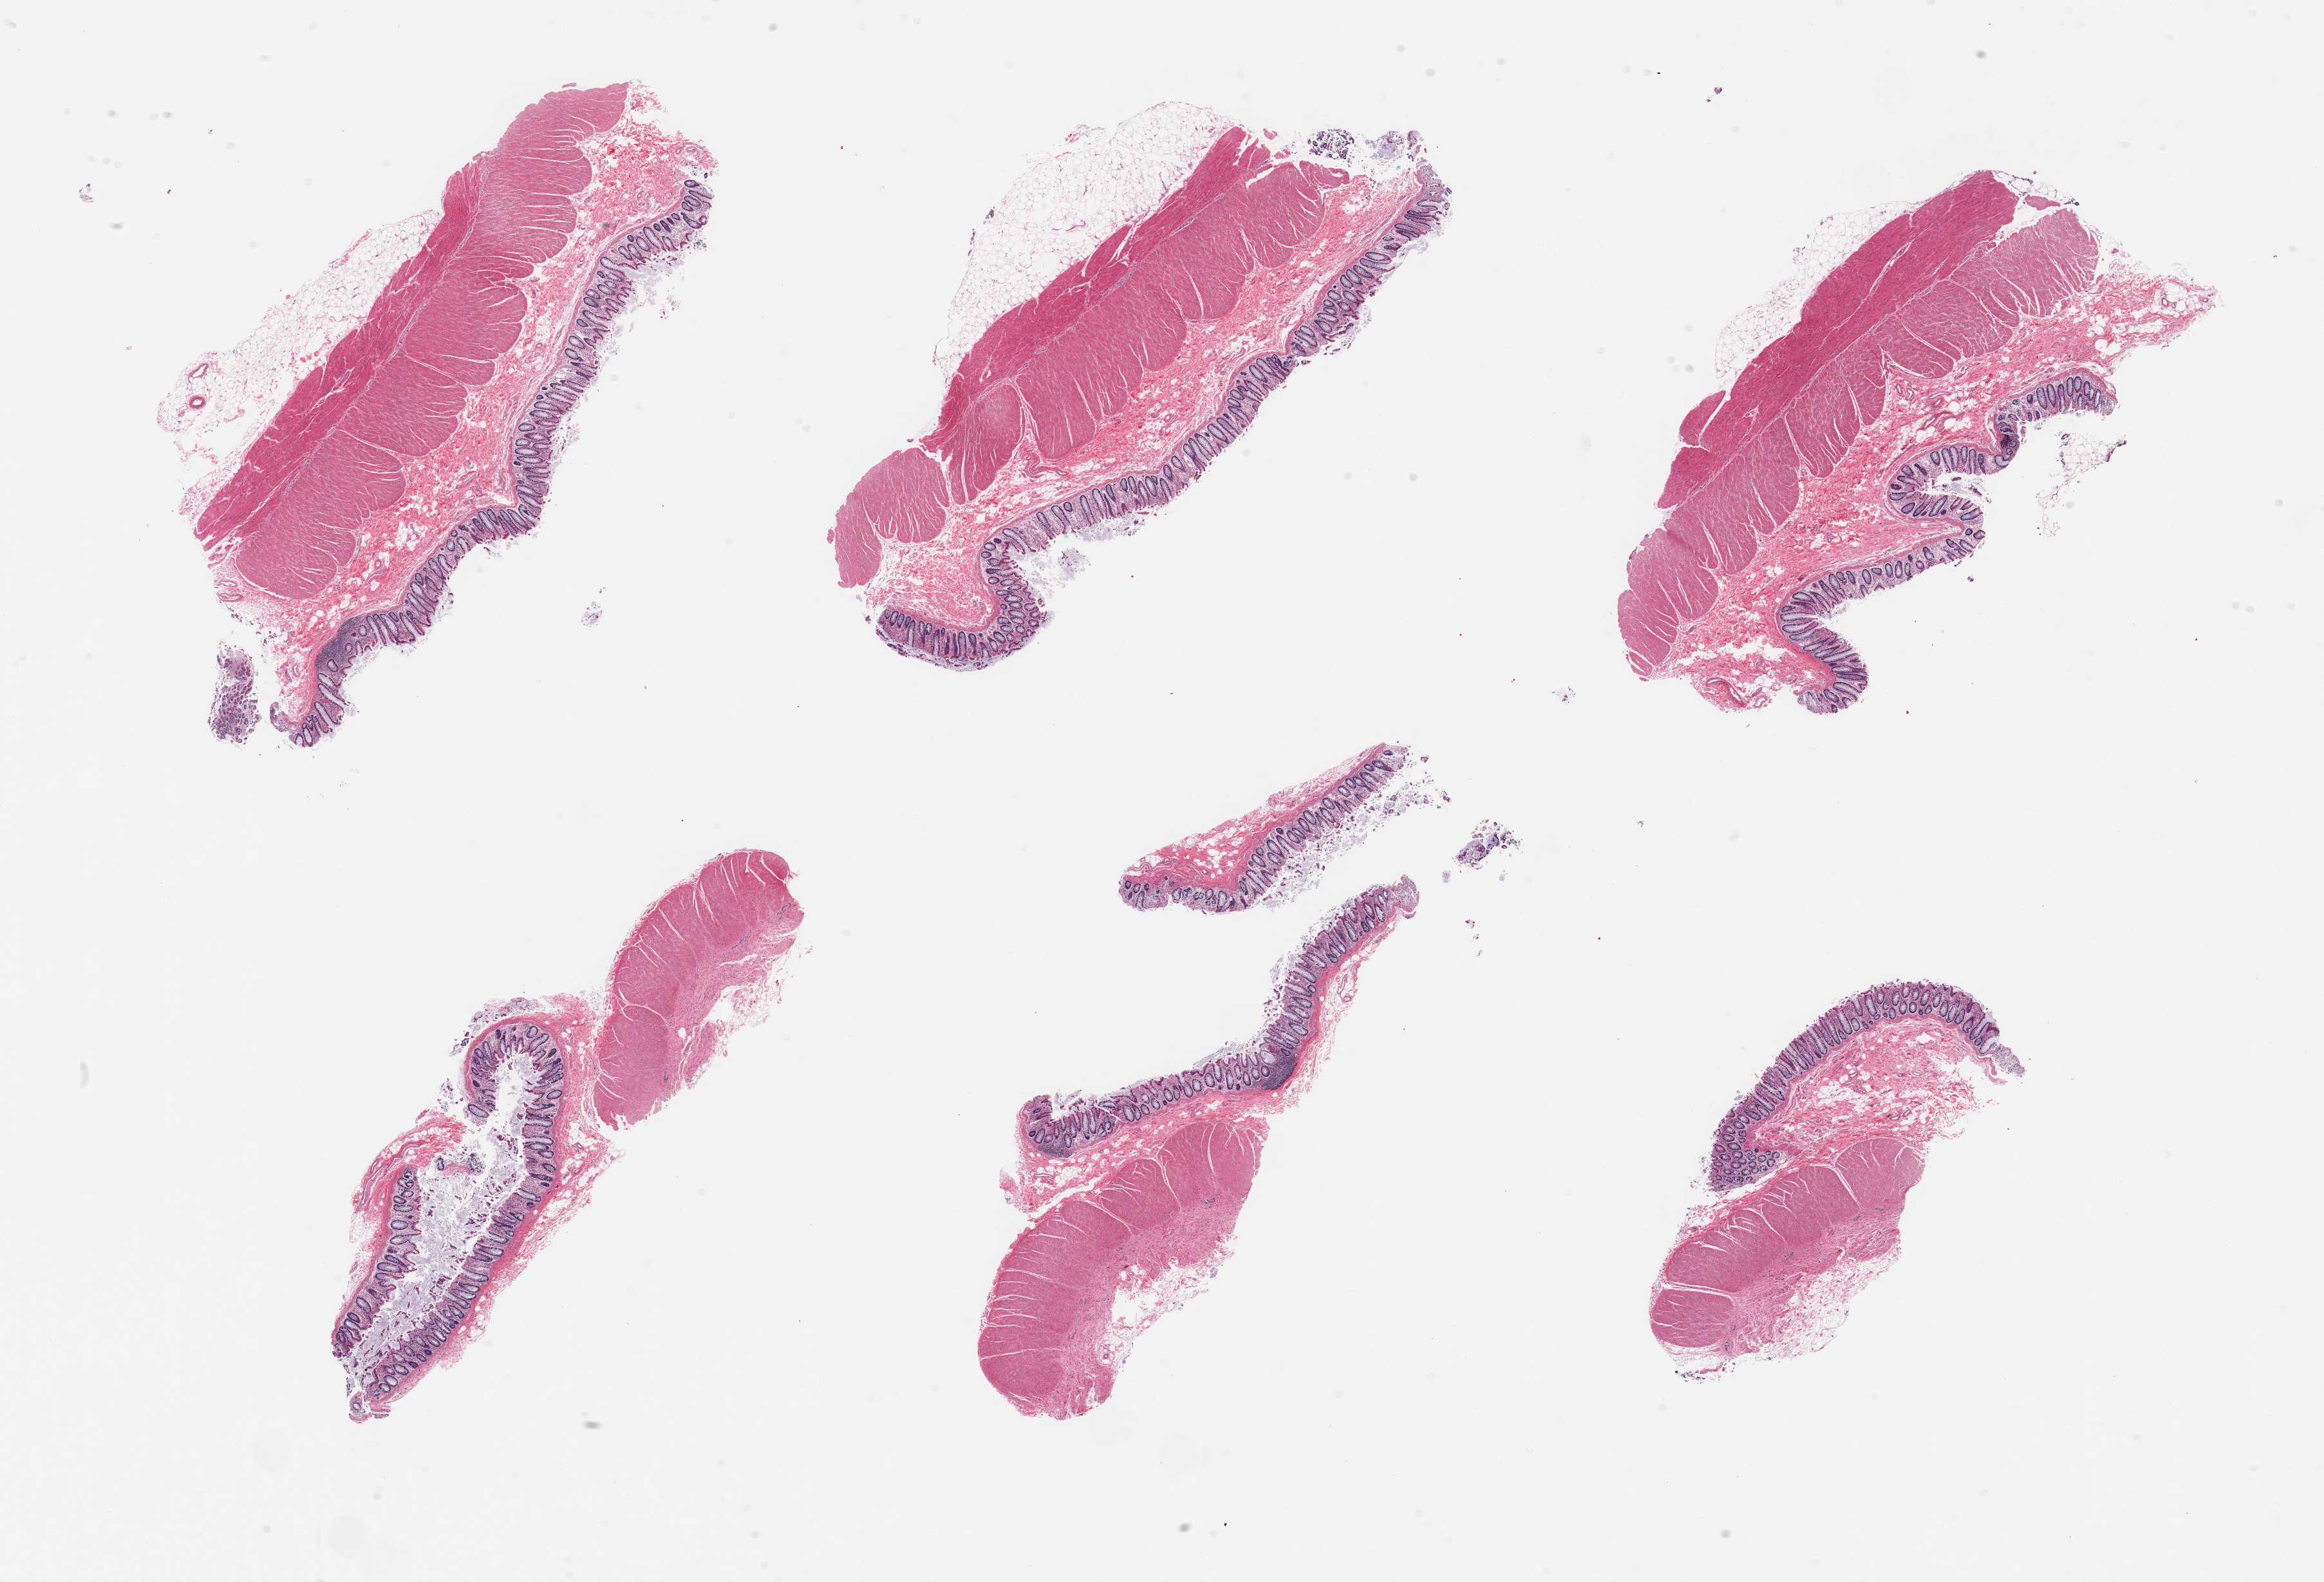
H&E whole-slide image, a low-resolution overview of the entire scanned area, about 28.5 x 19.4 mm, PAXgene-fixed paraffin-embedded (PFPE) section, sampled site (target tissue): sigmoid colon, donor tissue sample. Donor: male.
Pathologist's review note for this sample: 6 pieces; mild to moderate mucosal autolysis; target muscularis preserved.